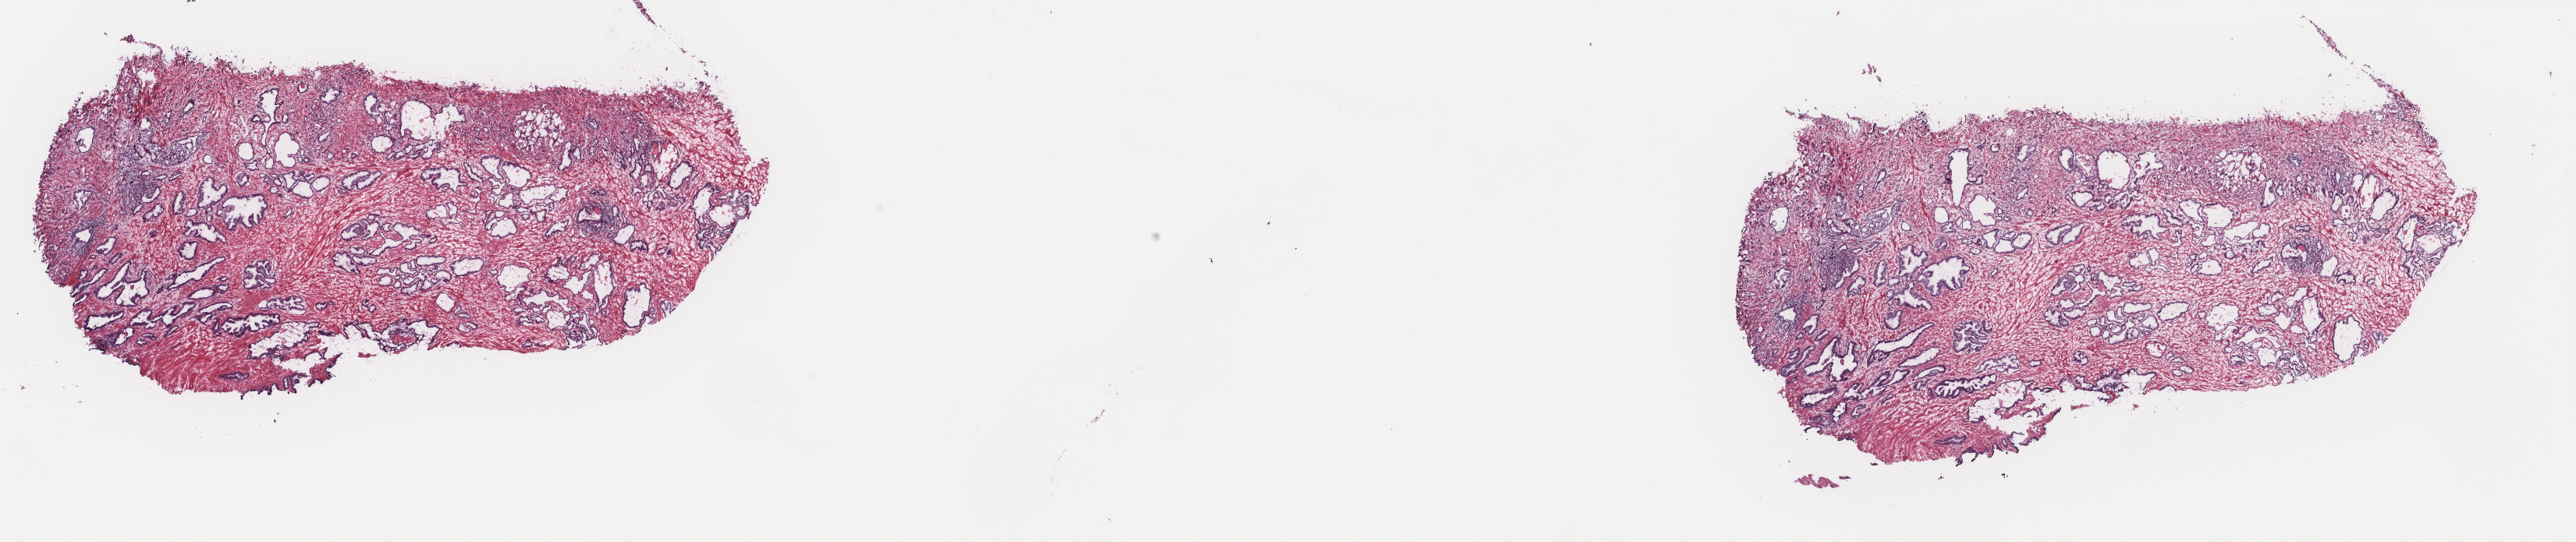
Whole-slide histology image, H&E, shown as a low-resolution overview of the whole scanned area (about 26.2 x 5.5 mm, slide scanned at 40x); frozen section from the top of the tissue portion; prostate, primary tumour sample. Male patient; age at initial diagnosis 68 years. Composition of this section per pathologist review: tumour cells 44%, tumour nuclei 80%.
Pathologic diagnosis: Adenocarcinoma, NOS.